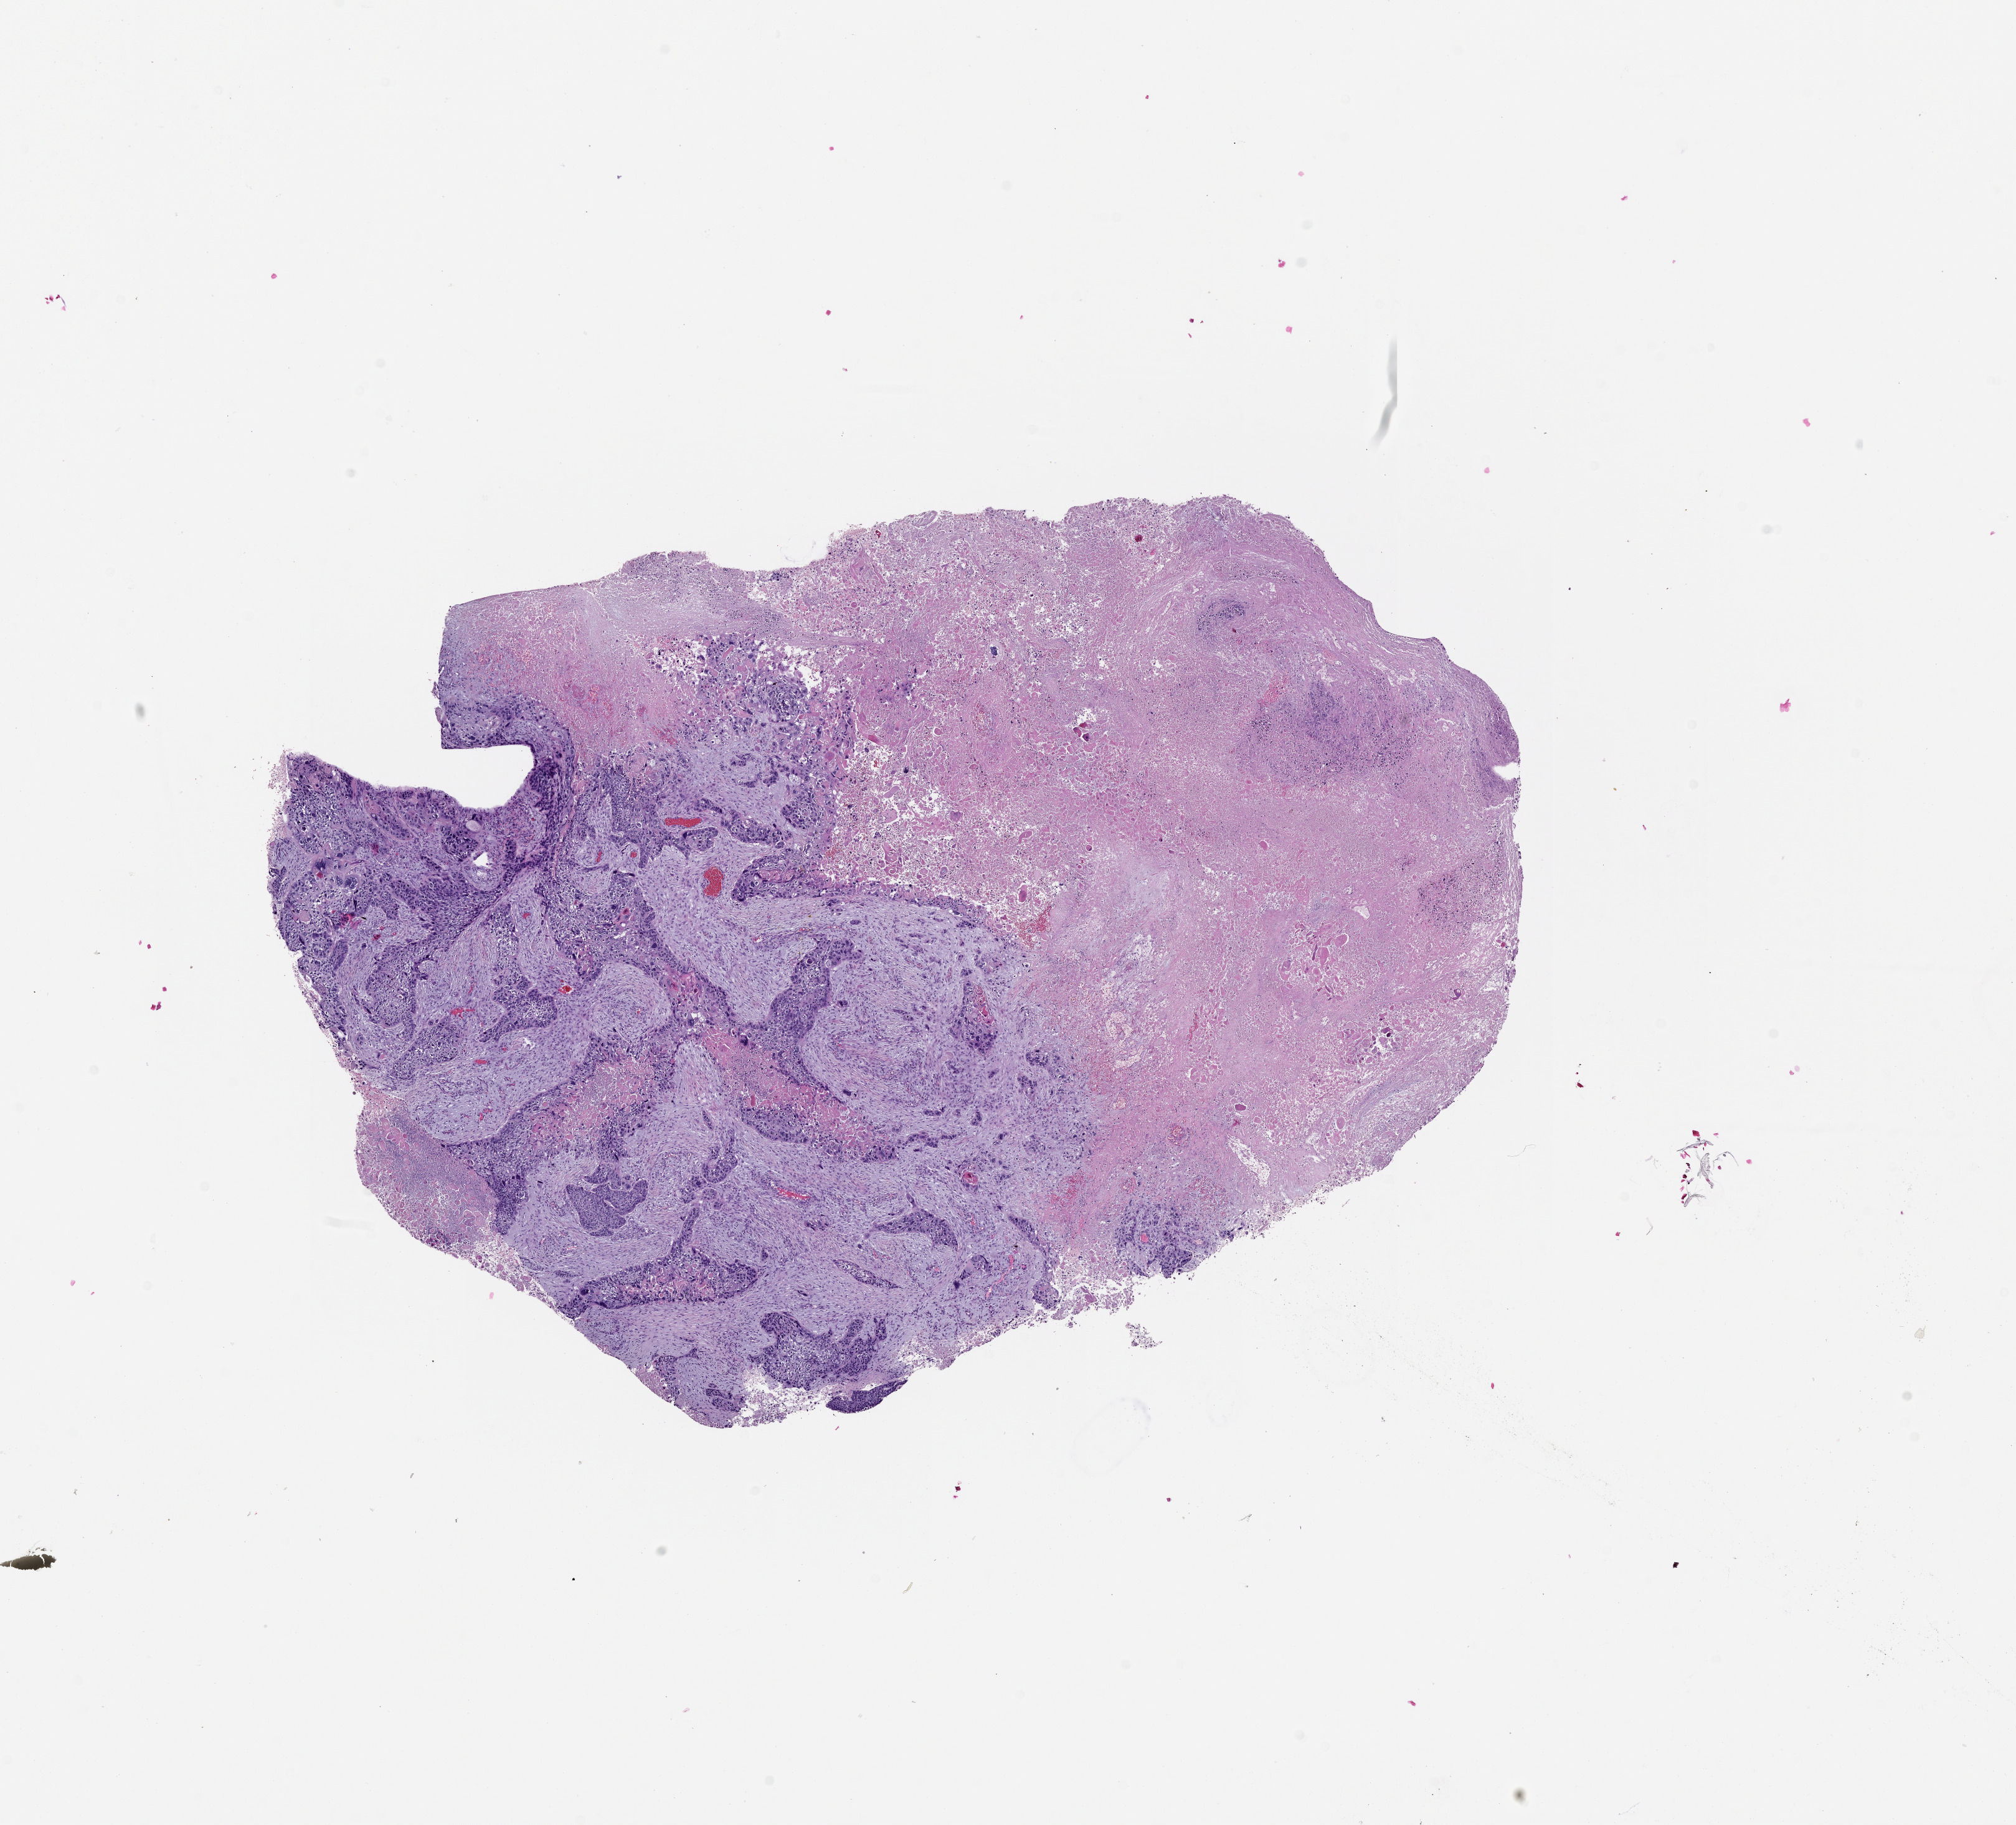
H&E-stained whole-slide image, whole scanned area (about 13.0 x 11.8 mm, acquisition: 20x scan) shown as a low-resolution overview, lung, tumour tissue. Patient: male, age 55 years.
Patient diagnosis (cohort enrolment): squamous cell carcinoma (lung).